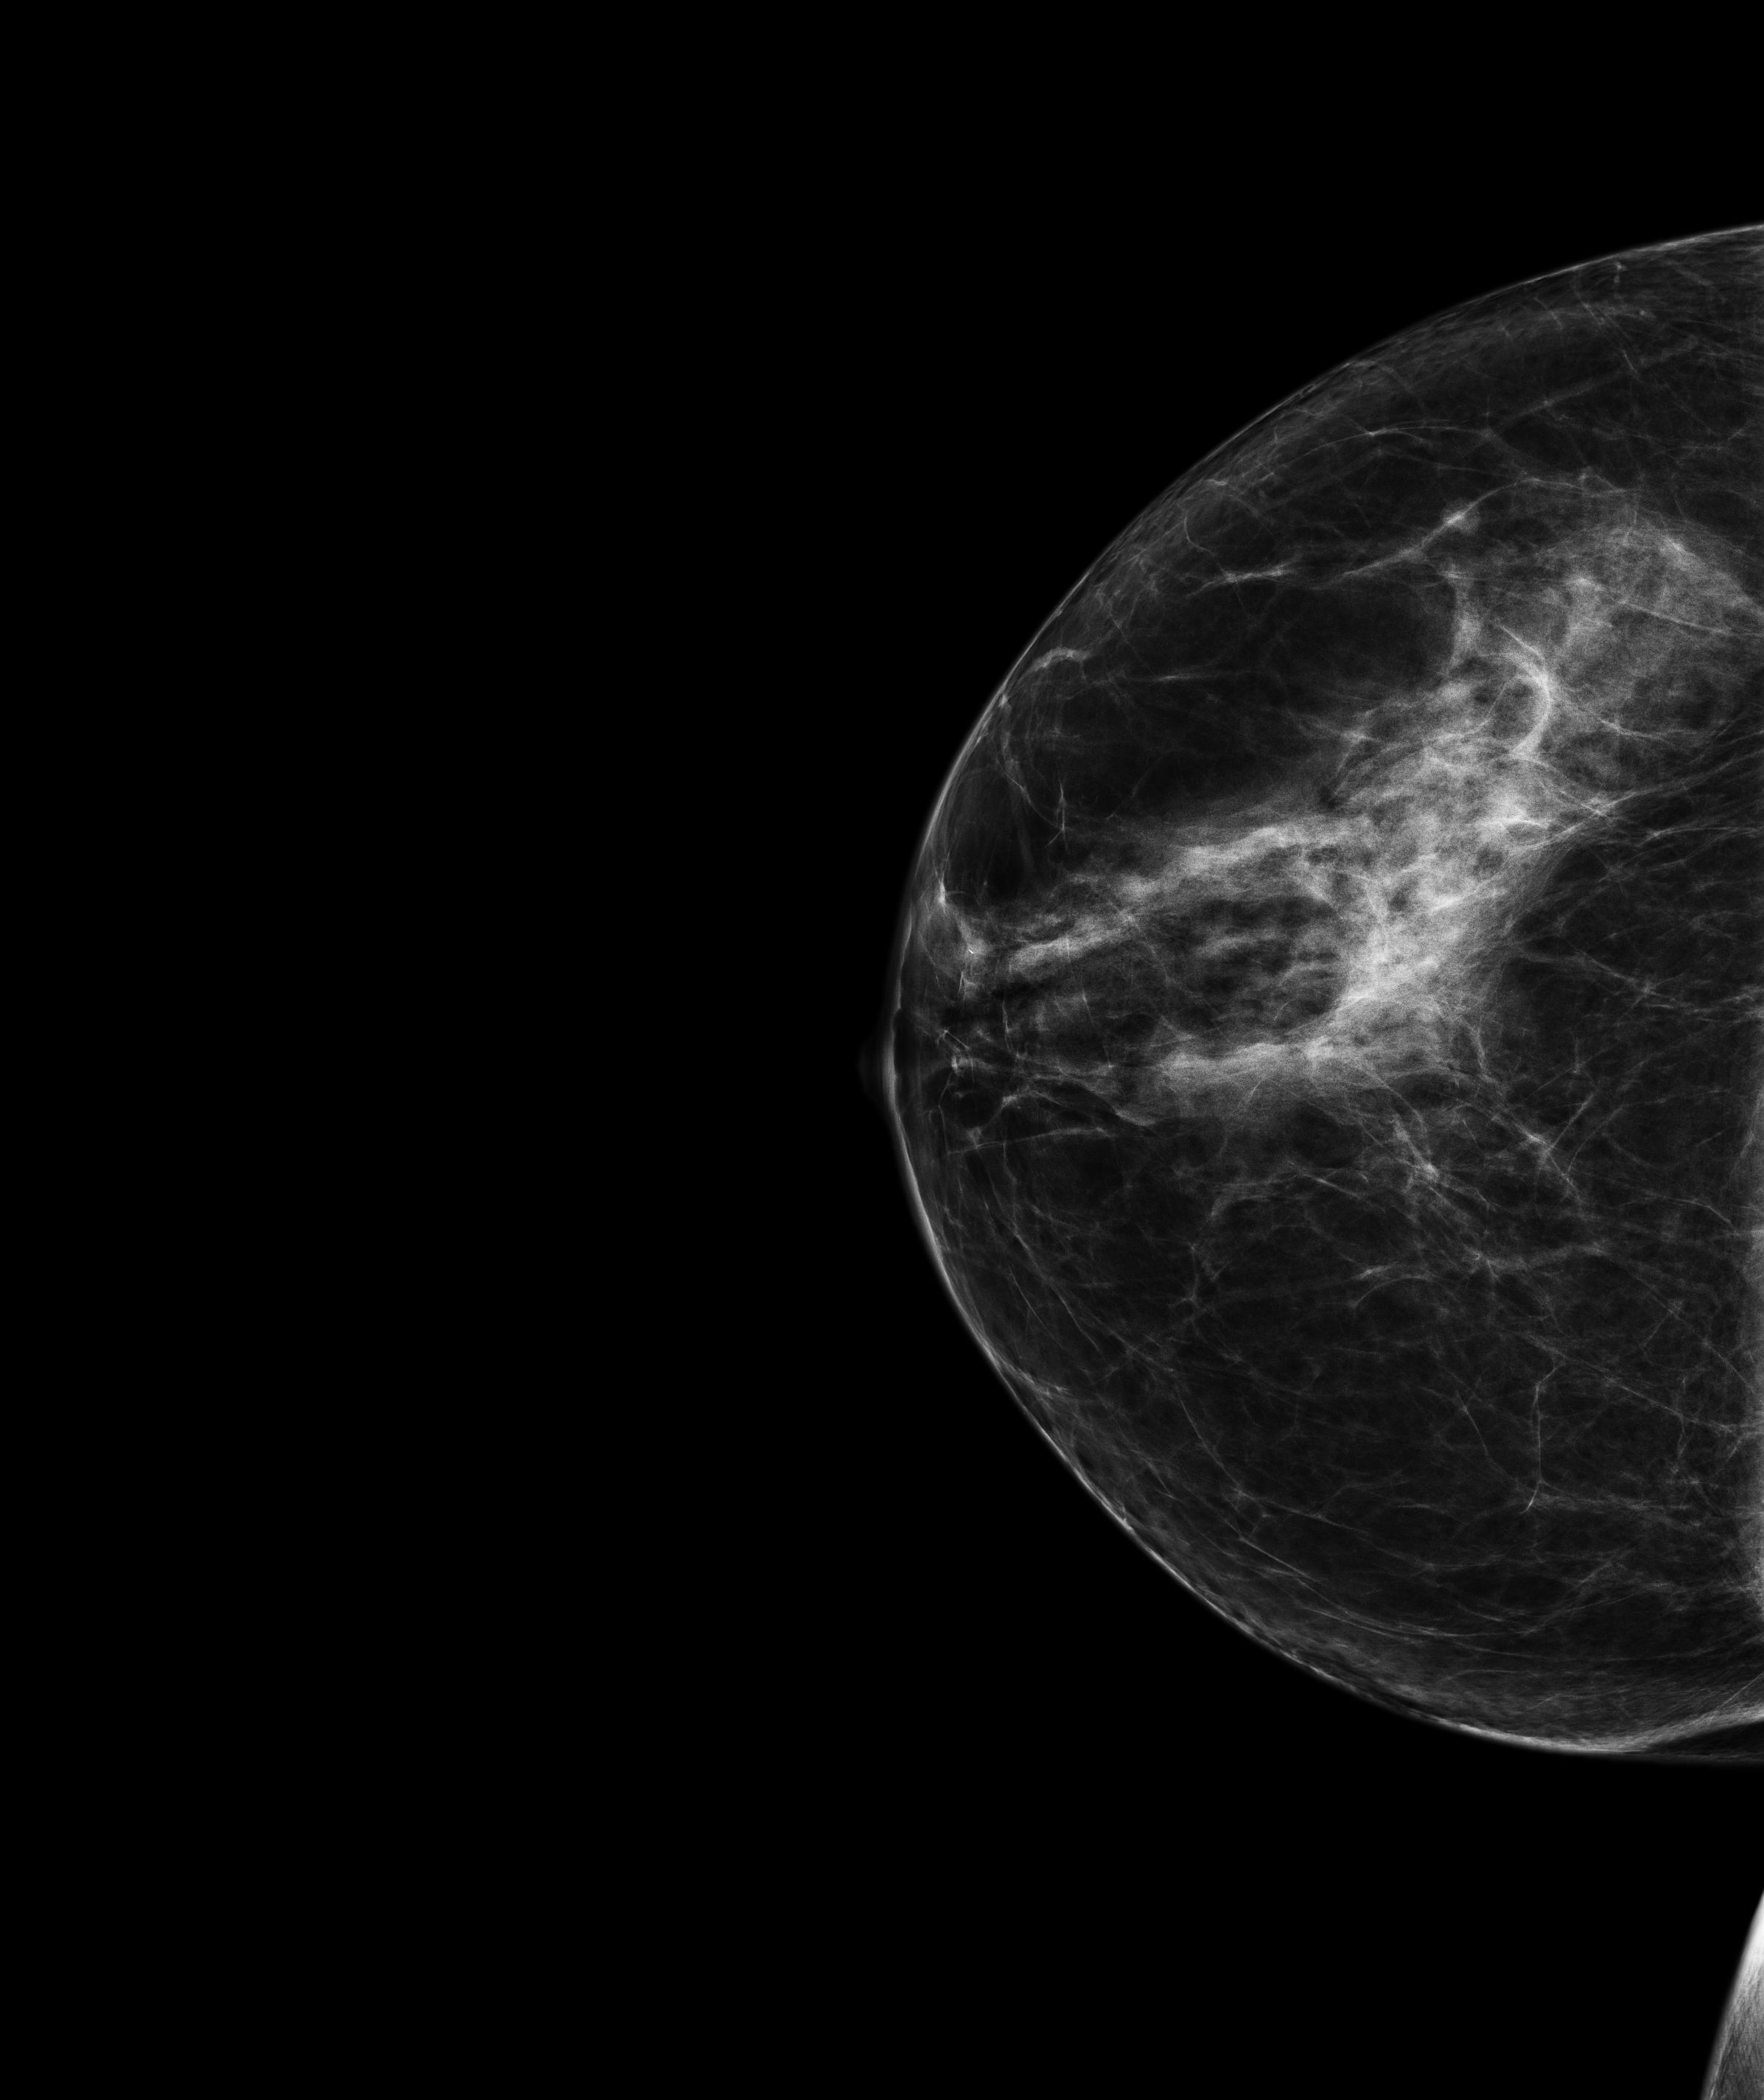
Annual screening mammography examination, compressed breast thickness 64.5 mm, system: Senographe Pristina. Patient aged 56 years (female).
Image type: full-field digital mammogram. Breast: right. Projection: craniocaudal (CC) view.